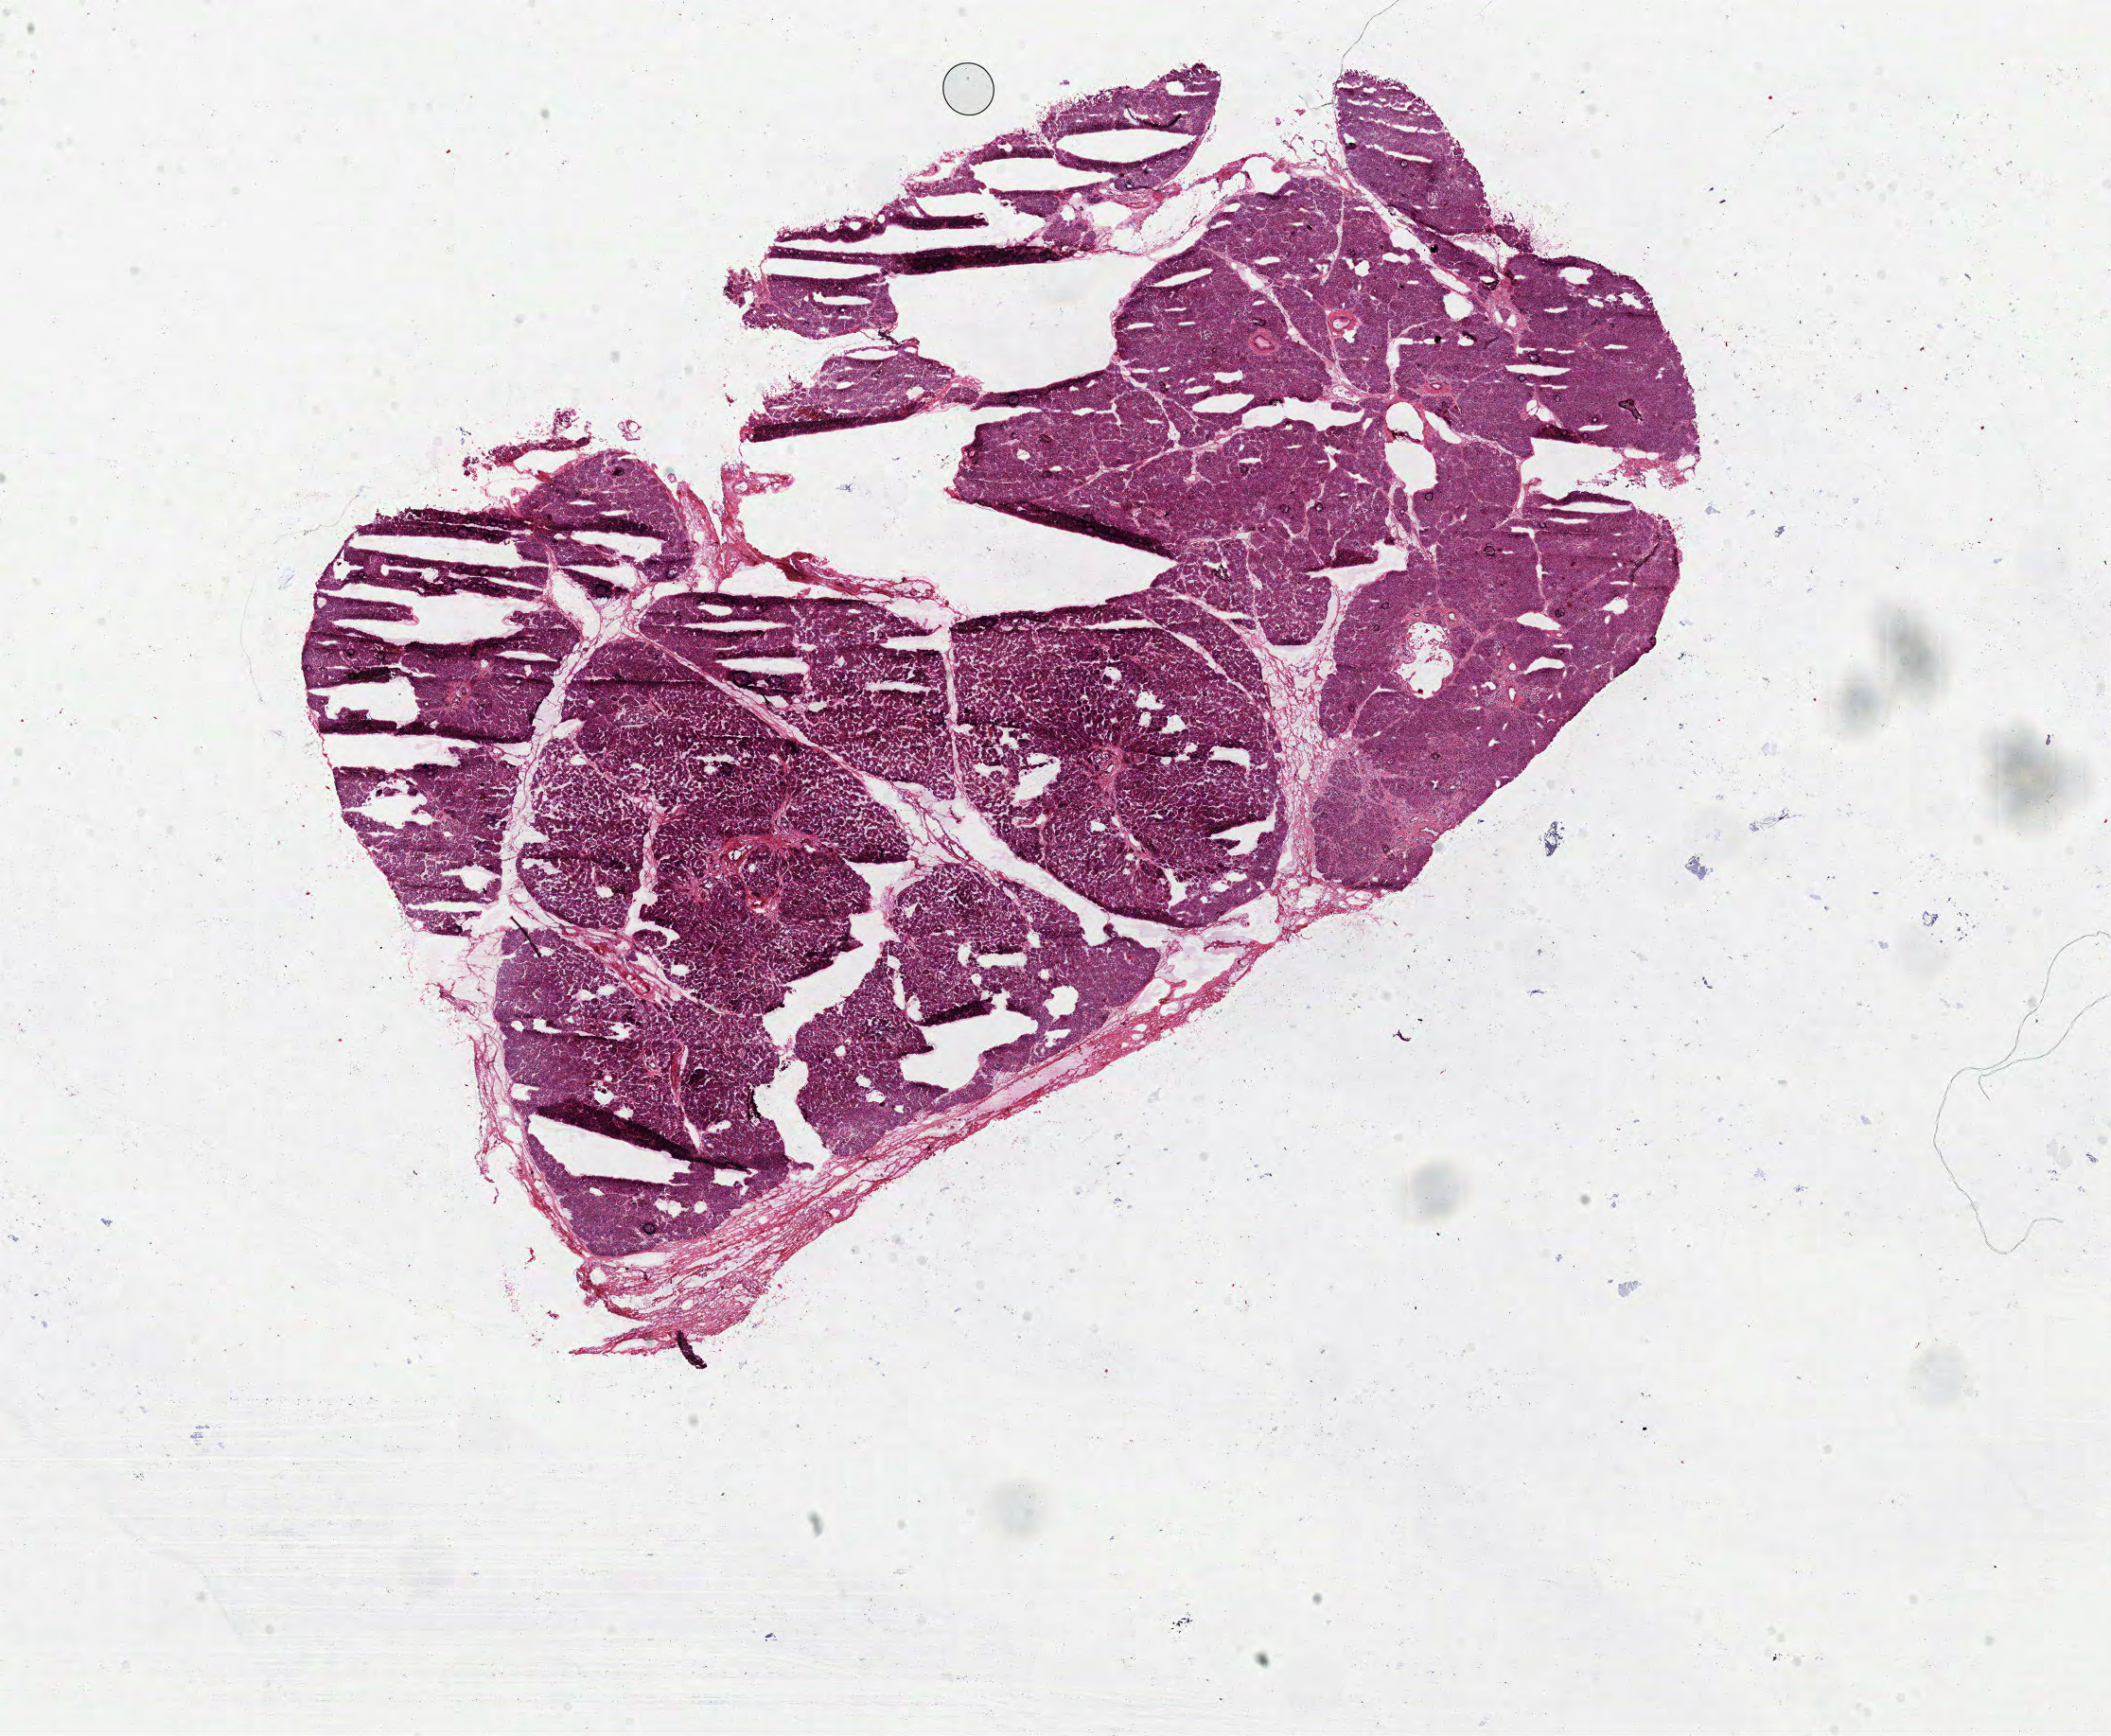
Digitized Hematoxylin and eosin (H&E) stained tissue section (whole slide) — shown as a low-resolution overview of the whole scanned area (about 17.6 x 14.5 mm, slide scanned at 40x), frozen section, pancreas, solid tissue normal (non-tumour tissue) sample. Male, age 52 years at initial diagnosis.
This section: solid tissue normal sample (biorepository sample class). Patient diagnosis: Infiltrating duct carcinoma, NOS.